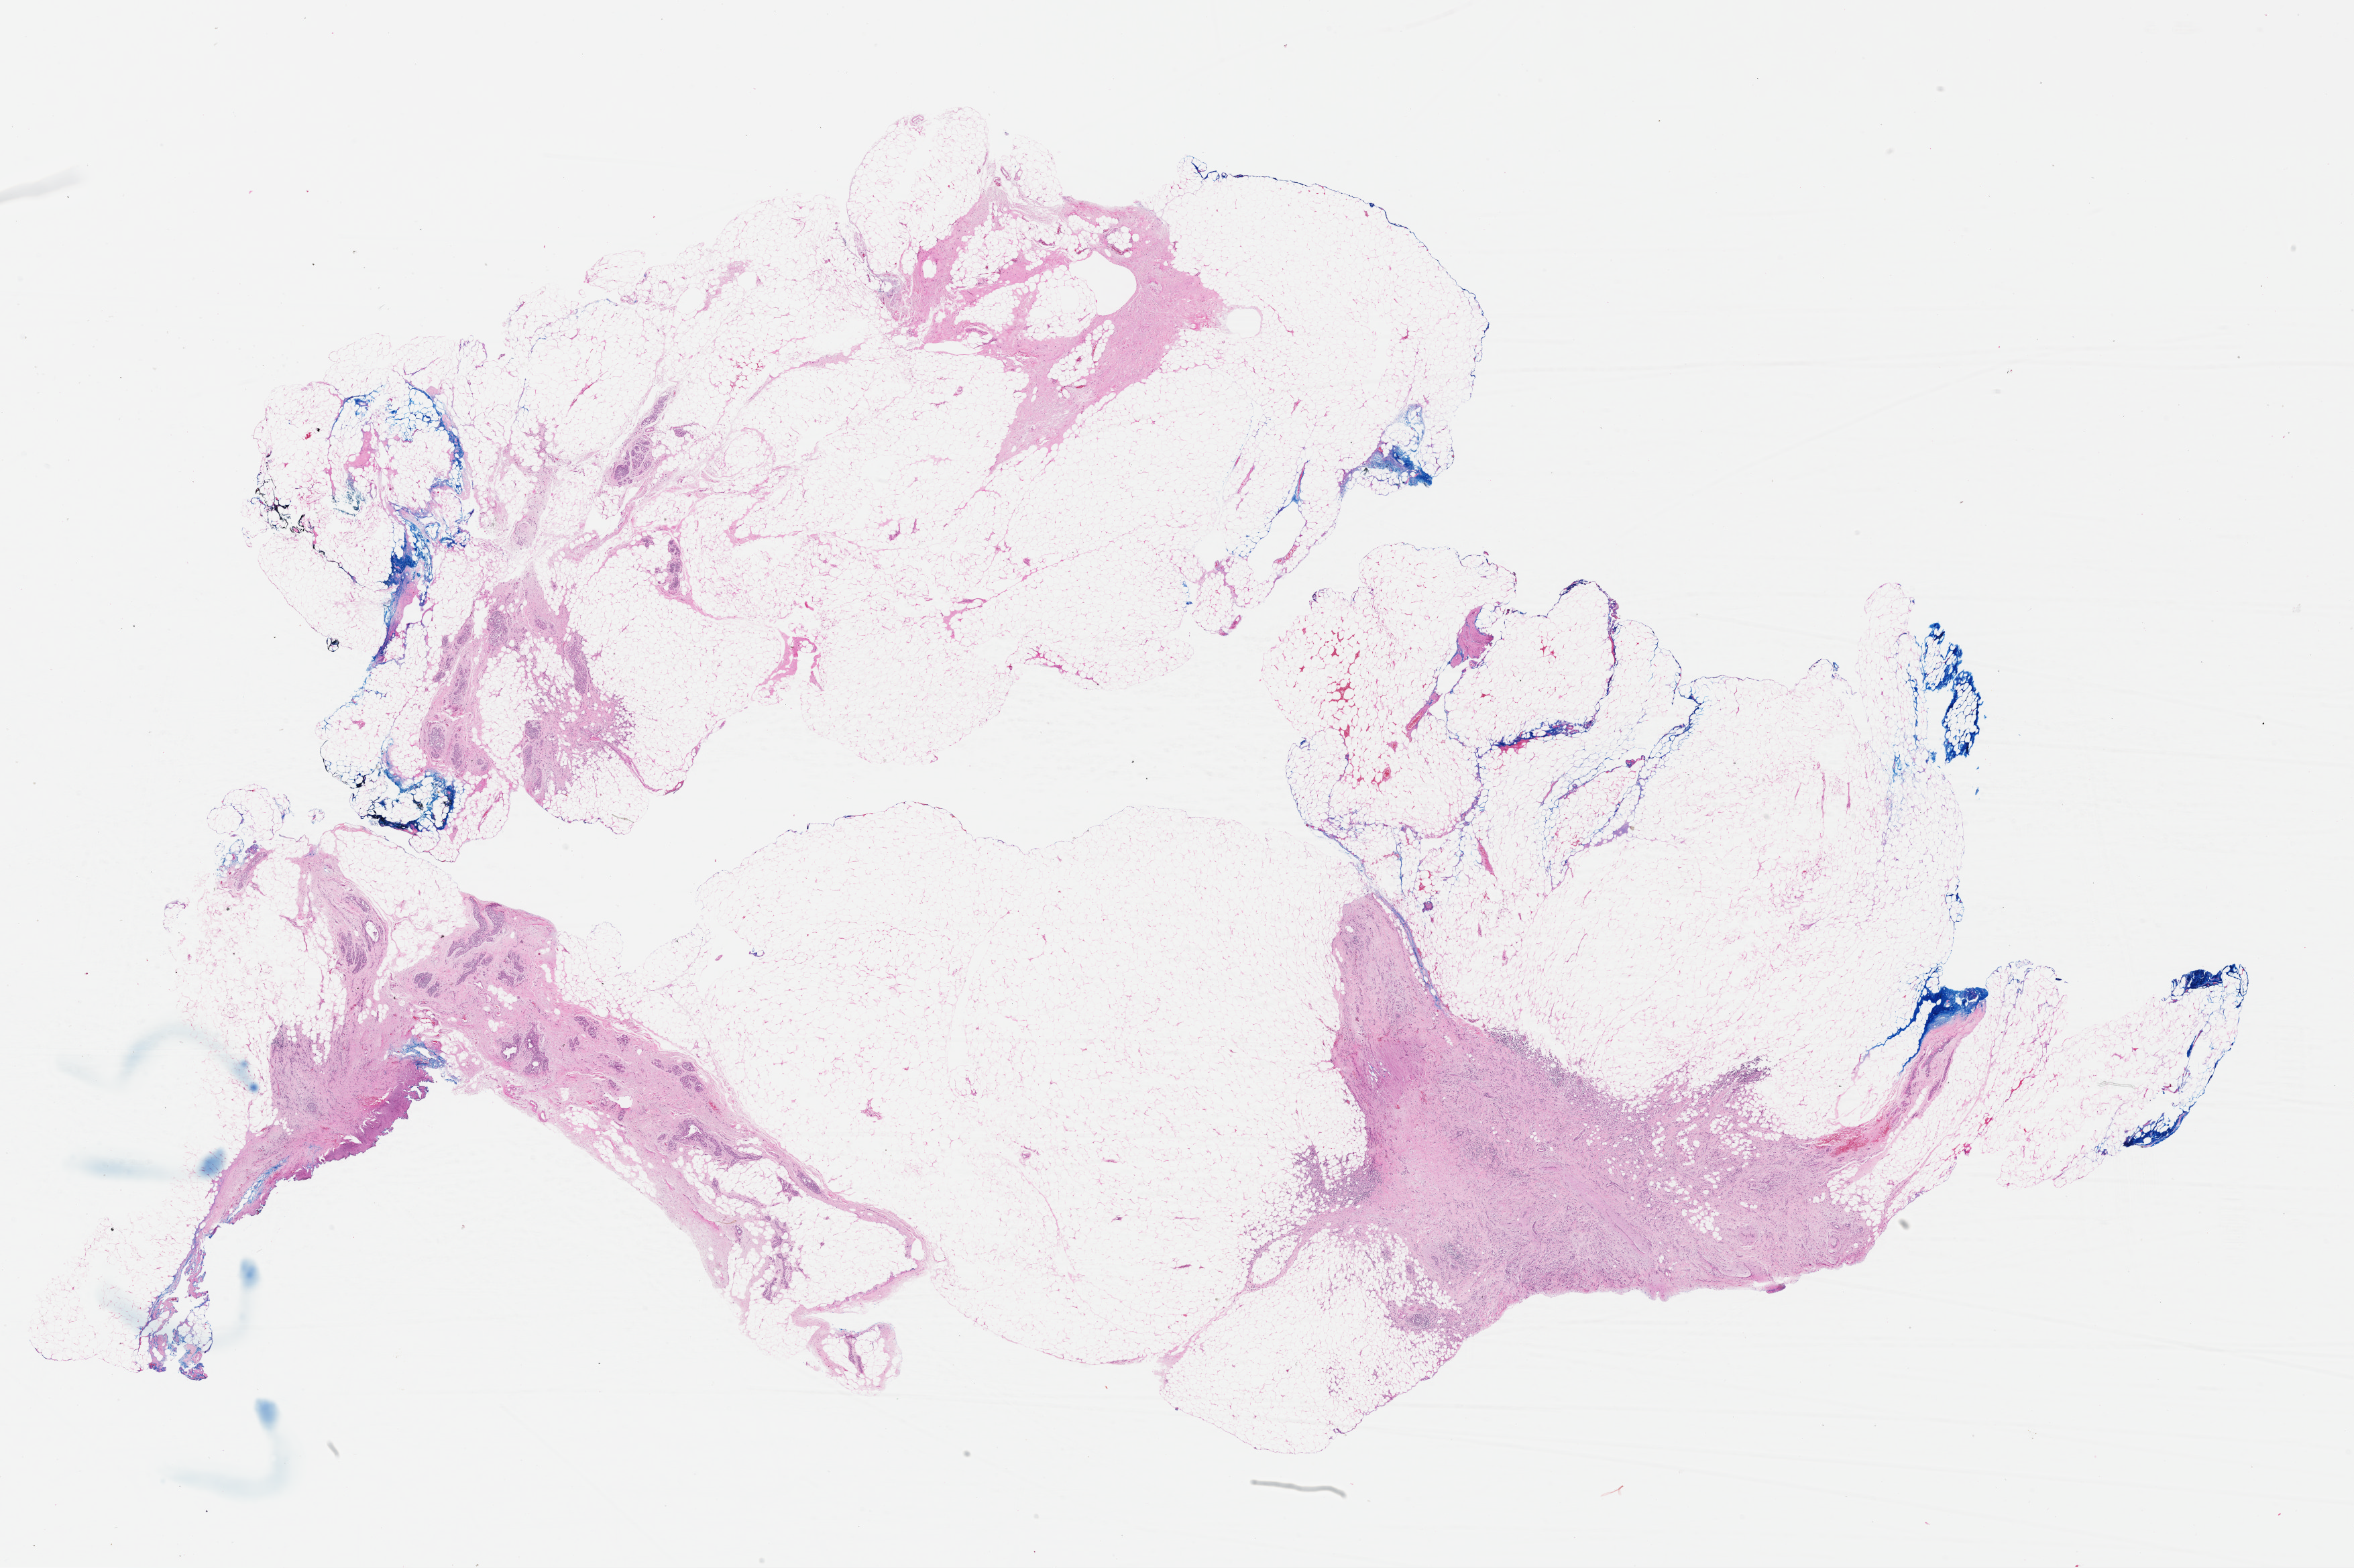
H&E-stained whole-slide image, low-resolution overview of the scanned area, about 27.6 x 18.4 mm. FFPE section. Sample: primary tumour, breast. Patient: female, age at initial diagnosis 56 years.
• AJCC pathologic stage: I (6th edition)
• TNM: T1 N0 (i+) M0
• diagnosis: Lobular carcinoma, NOS